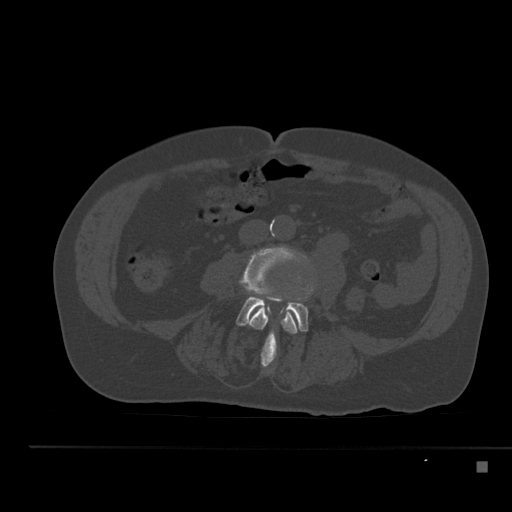
CT including the spine, one axial slice. Slice 152 of 517 in the series (ordered by position). 120 kVp. Bone window (W 1800 / L 400 HU). 1.5 mm slice thickness. 512 × 512 image matrix, field of view 408 × 408 mm. Male patient, age 70 years. From the clinical record (not read from this slice): primary cancer: renal.
Outlined on this slice (semi-automatic segmentation, software-assisted and operator-edited):
- L3 vertebra: bounding box <244,246,308,368> (left, top, right, bottom; pixels)
- L4 vertebra: <236,293,308,332>